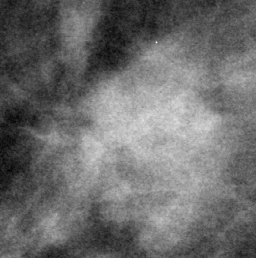
Region of interest cut from a scanned film mammogram (one marked finding), right breast, MLO view.
Marked abnormality: mass, shape irregular / architectural distortion, margins microlobulated / ill defined / spiculated; BI-RADS assessment category 4; subtlety rating 4 on a 1 (subtle) to 5 (obvious) scale; pathology result (as recorded, not read from the image): malignant.